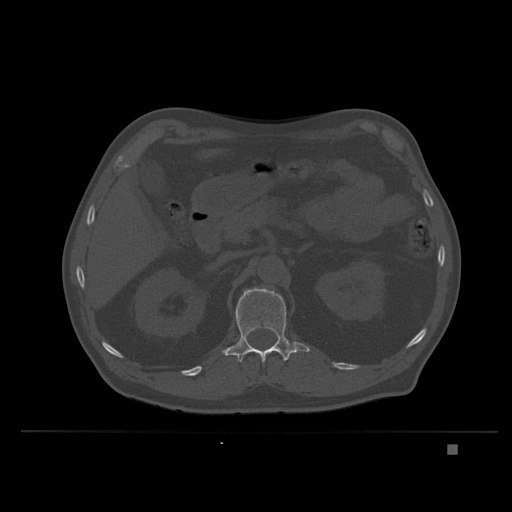
CT including the spine, one axial slice; slice 140 of 435 in the series (ordered by position); bone window (W 1800 / L 400 HU); 512 × 512 image matrix, field of view 434 × 434 mm. Patient: male, 73 years. From the clinical record (not read from this slice): primary cancer: skin.
Annotated regions visible in this slice (semi-automatic segmentation, software-assisted and operator-edited):
- L1 vertebra: bounding box <222,288,310,363> (left, top, right, bottom; pixels)